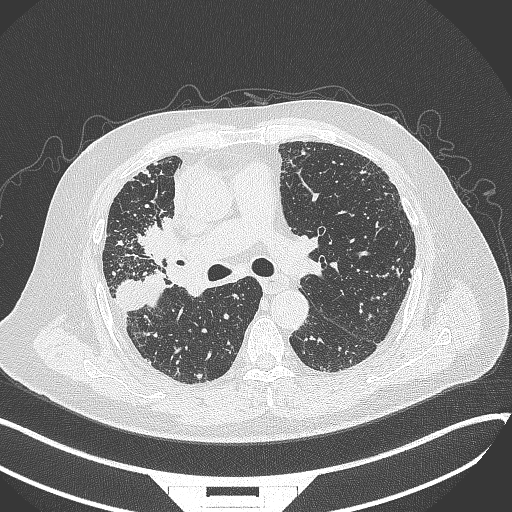
Chest CT, one axial slice; slice 208 of 384 in the series (ordered by position); 120 kVp; lung window (W 1500 / L -600 HU); 1 mm slice thickness; 512 × 512 image matrix, field of view 400 × 400 mm. Patient: male, 69 years. From the clinical record (not read from this slice): clinical TNM (as recorded): T4 N3 M1.
Annotated regions visible in this slice (bounding box drawn by a radiologist):
- lung tumour (recorded histology: adenocarcinoma): bounding box <129,216,188,265> (left, top, right, bottom; pixels)